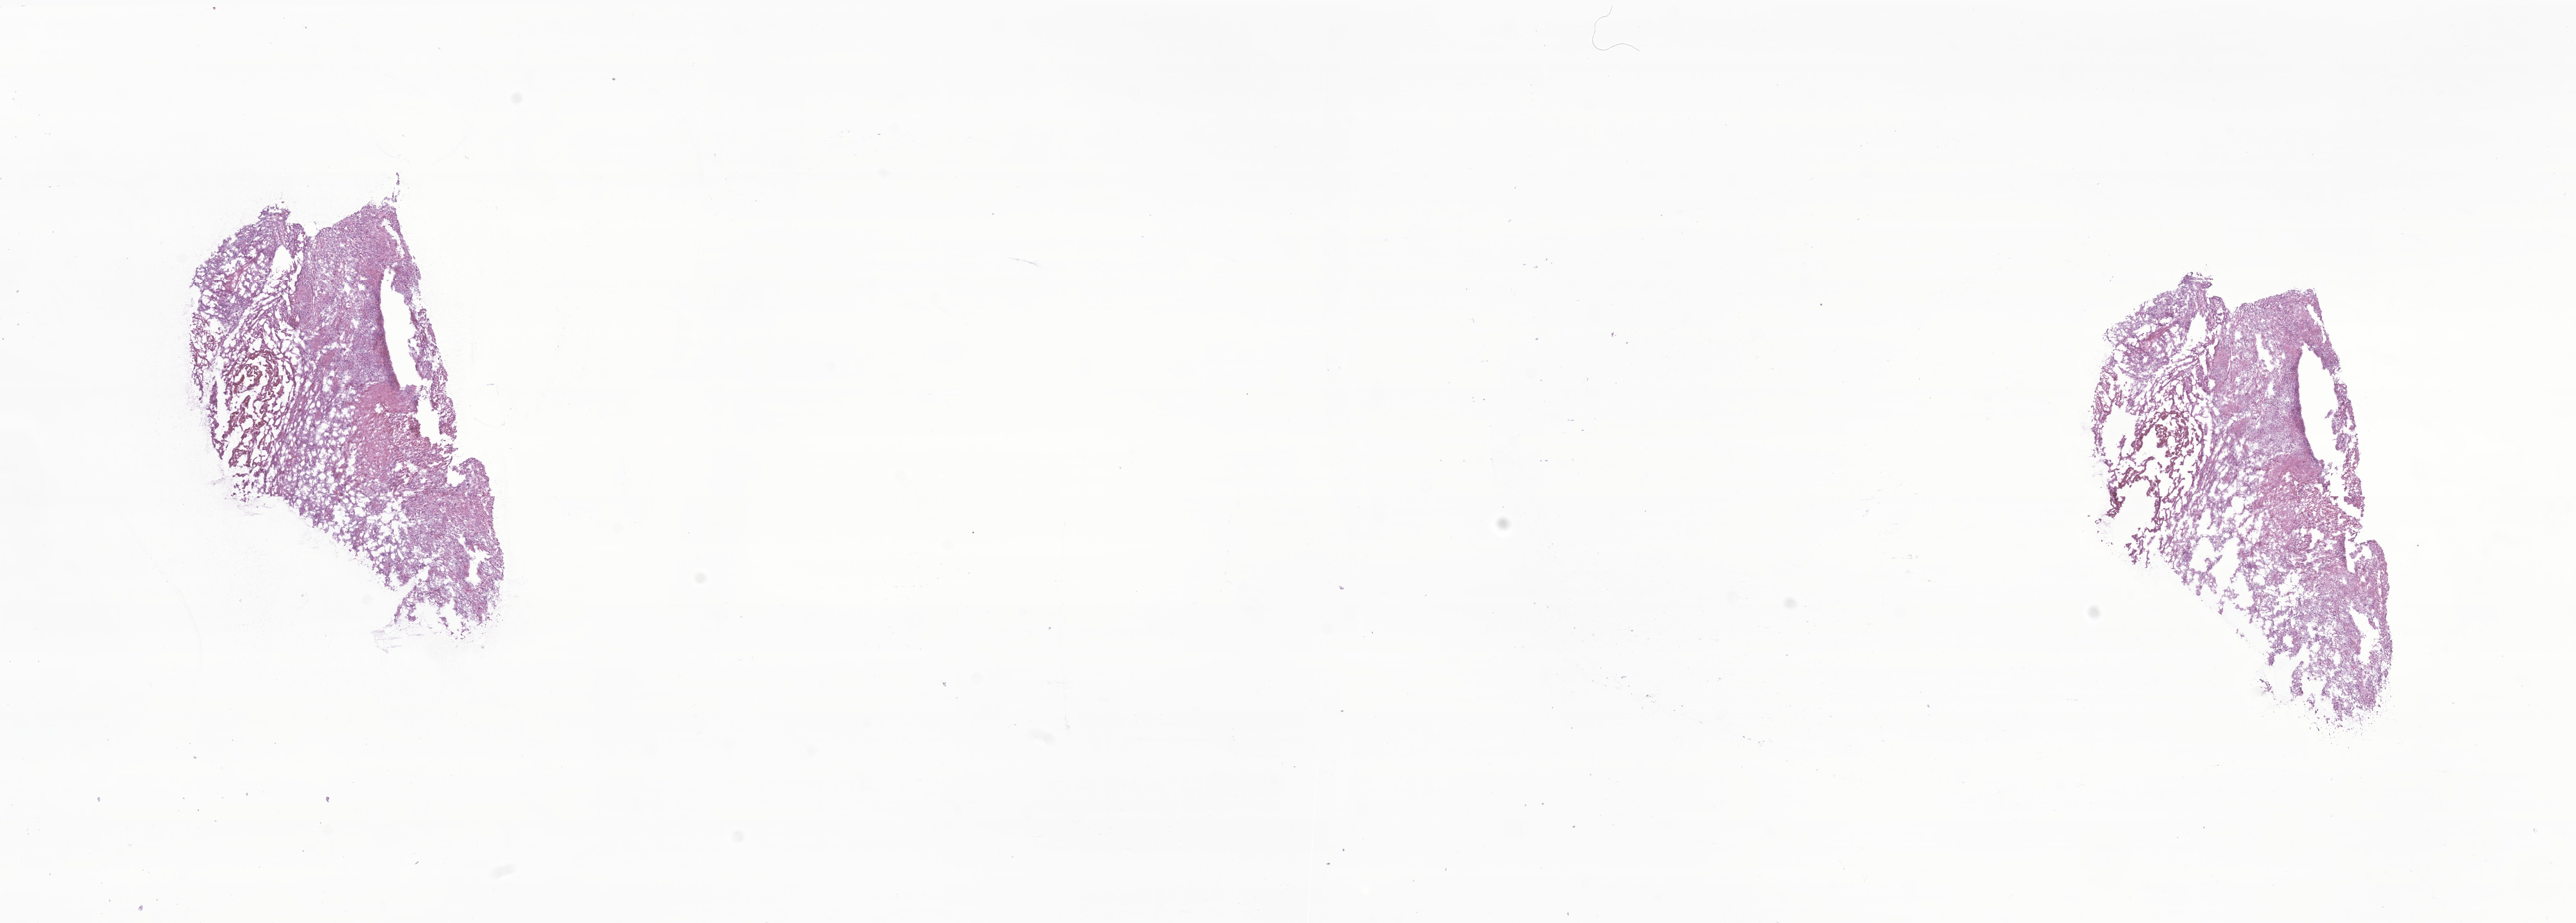
Haematoxylin and eosin whole-slide image of tumor tissue from the brain — shown as a low-resolution overview of the whole scanned area (about 25.4 x 9.1 mm); frozen section (OCT-embedded). Patient female; age 128 months (10 years 8 months).
Diagnosis: Pilocytic astrocytoma.